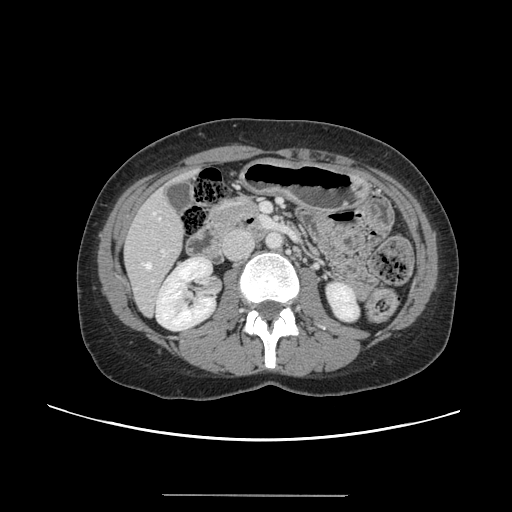
Contrast-enhanced abdominal CT, one axial slice. Slice 49 of 144 in the series (ordered by position). Soft-tissue window (W 400 / L 40 HU). 2.5 mm slice thickness. 512 × 512 image matrix. Female patient, age 53 years. Case-level facts recorded for this patient, not image findings: diagnosis: colorectal cancer liver metastases, imaged before liver resection; multiple liver metastases: yes; largest metastasis: 1.1 cm.
Outlined on this slice (manually delineated by an expert):
- hepatic veins: bounding box <146,213,160,269> (left, top, right, bottom; pixels)
- liver: <126,192,184,315>
- planned liver remnant (the part of the liver to remain after resection): <126,174,188,314>
- portal vein (with intrahepatic branches): <151,249,166,283>